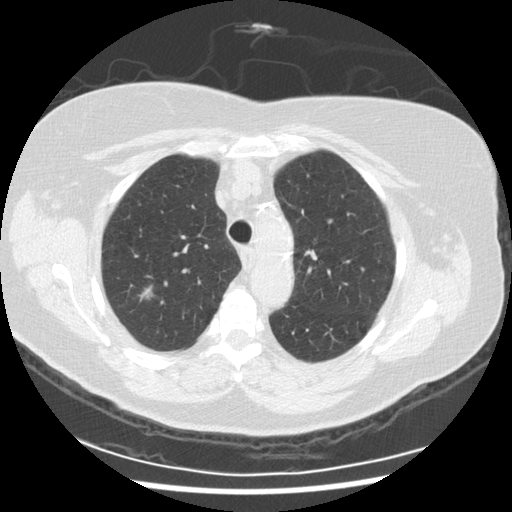
Low-dose screening chest CT, one axial slice; position 199 of 254 along the scan axis; lung window (W 1500 / L -600 HU); 512 × 512 image matrix, field of view 360 × 360 mm.
Outlined on this slice (outlined manually by an expert reader):
- lesion 1 (tumor, upper lobe of right lung): bounding box <139,287,153,301> (left, top, right, bottom; pixels)